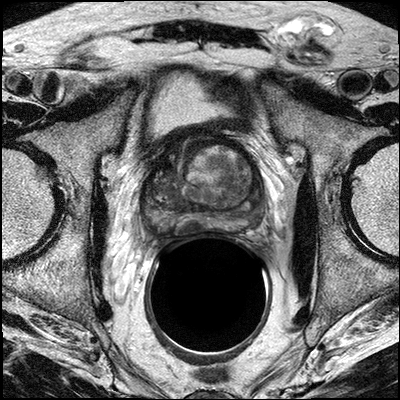
Prostate MRI examination; 3 images, each a single mid-volume slice chosen by position (not for content). Treatment context recorded for this patient: No Biopsy and surgery, patient is recommended for surgery.
Image 1: T2-weighted axial slice, series "T2W_TSE_AX", slice 17 of 32.
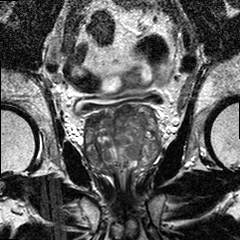
Image 2: coronal T2-weighted image, series "T2W_TSE_COR", slice 18 of 34, 3 mm slice thickness.
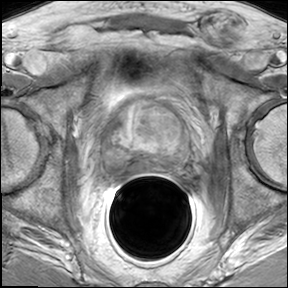
Image 3: axial dynamic contrast-enhanced (DCE) T1-weighted image, slice 17 of 32, dynamic phase 5 of 8, 6 mm slice thickness.
MRI report (verbatim):
The zonal anatomy is preserved. The prostate measures in the max. transverse diameter 5.3 cm, and maximal AP diameter 3.8 cm. The max. cranial caudal diameter is 4.8 cm. This results in an estimated gland volume of 50 cc. There are multiple suspicious geographic areas of hypo intense signal on the T2 weighted images seen scattered throughout the entire prostate, including in the central gland, and left and right peripheral zones of both sides and involving base mid third and apex. In these areas there is also suspicious rapid wash-in and wash-out seen on the dynamic contrast enhanced series. A indistinct or partially thickened and irregular pseudo-capsule is seen on the T2 weighted images between the 7 and 8 o'clock position at school, at the middle 3rd of the prostate towards the right neuro vascular bundle. However there are no manifest tumor mass is seen beyond the capsule; irregularity in morphology and atypical enhancement is seen within the fibro-muscular band. Again no manifest tumor extension beyond the gland borders is seen. No involvement of the left neuro-vascular bundle. No definite involvement of the right neuro-vascular bundle. The seminal vesicles are thin walled and show regular T2 hyperintense intraluminal signal; no enhancement on the DCE images. There is no pelvic lymphadenopathy seen. IMPRESSION:1. Multifocal bilateral prostate cancer within the central gland and left and right peripheral zones with possible capsular infiltration especially right posterior lateral (7-8 o'clock and anteriorly (11-1 o'clock. No manifest extraprostatic extension. No seminal vesicals infiltration. No pelvic lymphadenopathy .